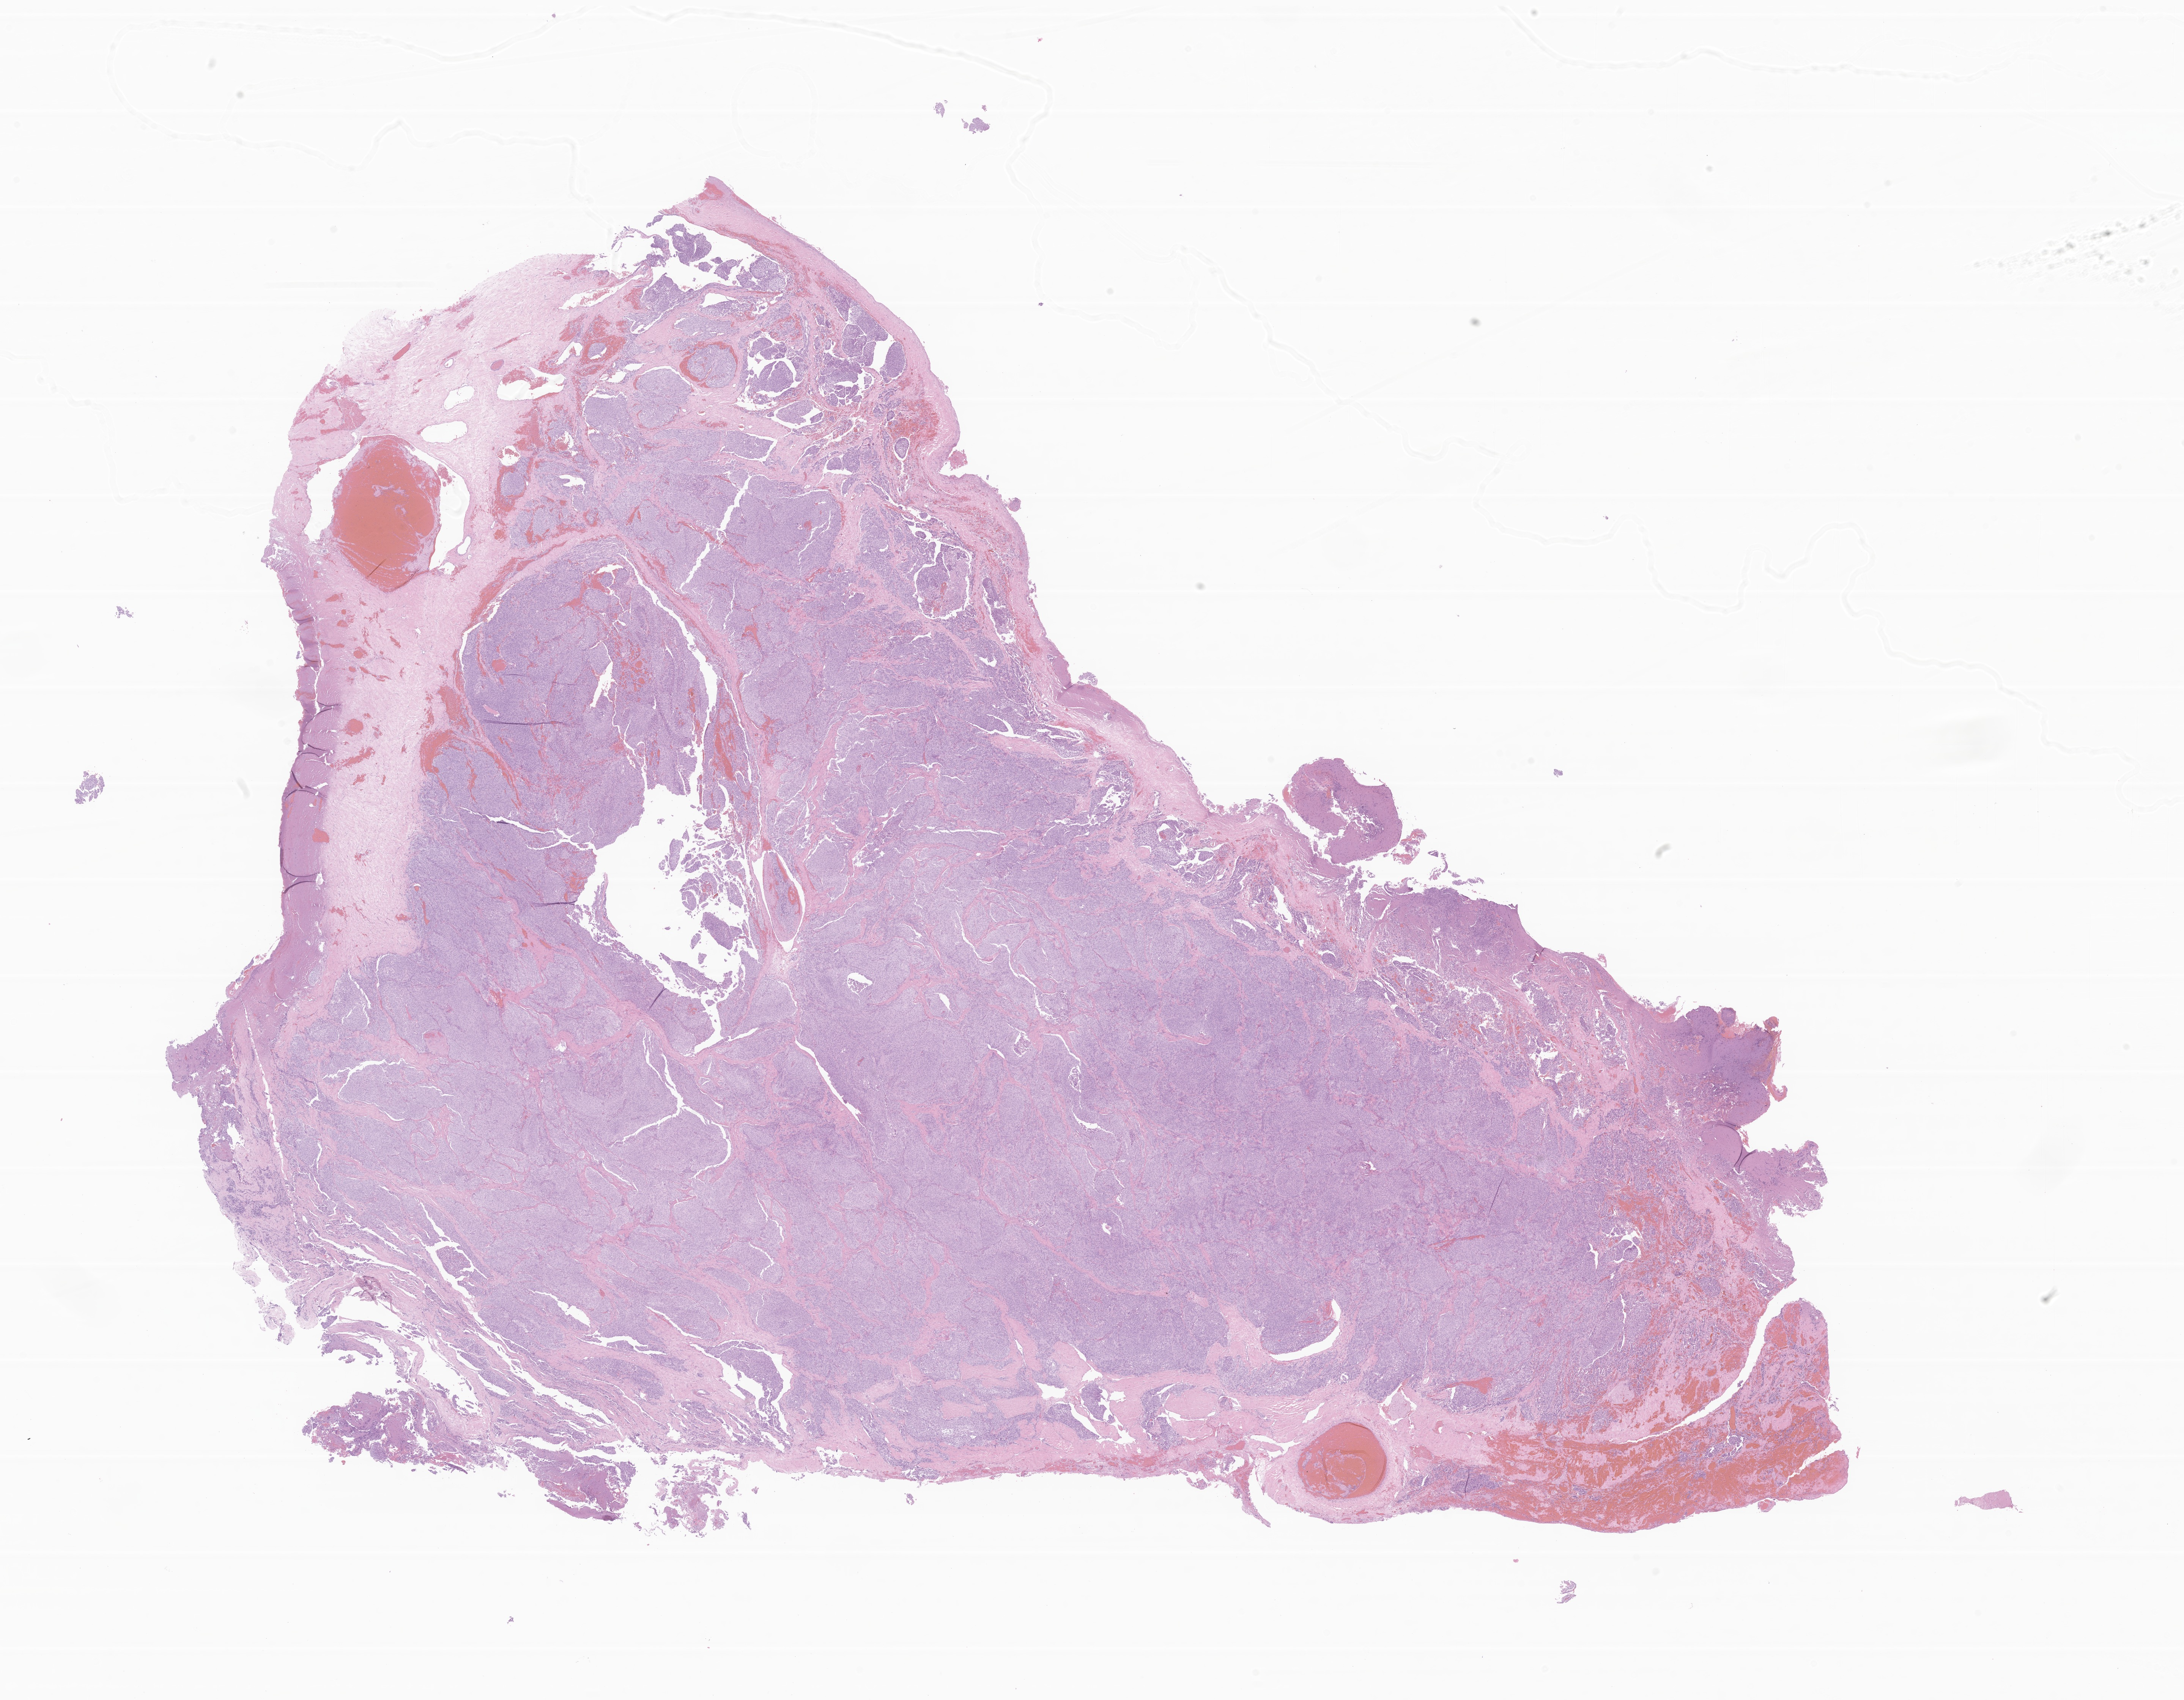
Whole-slide image, hematoxylin and eosin (H&E) stain of tumor tissue from the brain — low-resolution overview of the scanned area, about 24.3 x 18.9 mm, formalin-fixed paraffin-embedded section. Patient: male, age 171 months.
Diagnosis (ICD-O-3 morphology term): Meningioma, NOS.